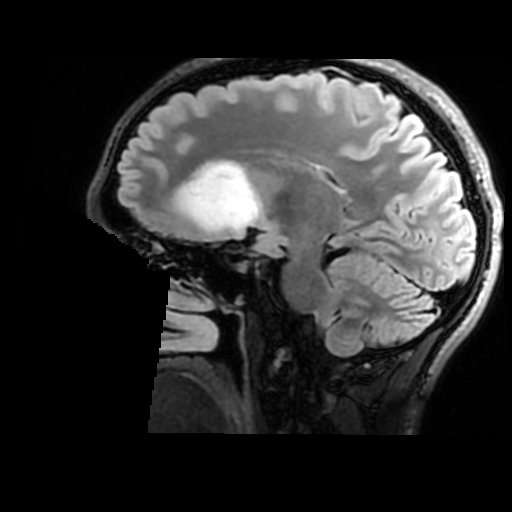
Brain MRI from a brain-tumour surgery series, one sagittal slice. Position 101 of 176 along the scan axis. T2 FLAIR. 512 × 512 image matrix, field of view 240 × 240 mm. From the clinical record (not read from this slice): histopathology: Astrocytoma; WHO grade: 2; IDH mutation: yes.
Structures marked on this image (outlined manually by an expert reader):
- tumour: bounding box [x1, y1, x2, y2] px = [179, 160, 260, 232]